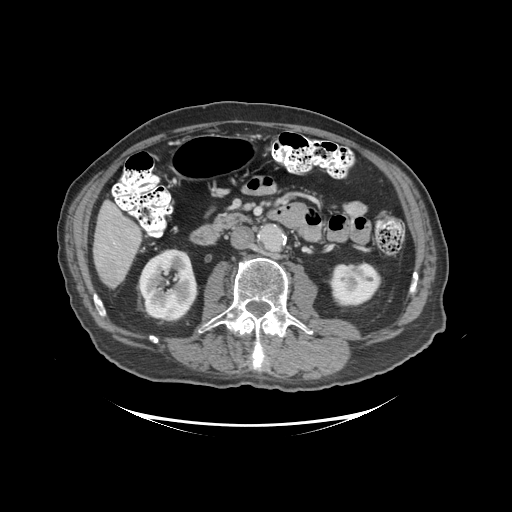
Contrast-enhanced abdominal CT (liver protocol), one axial slice. Position 33 of 99 along the scan axis. Reconstruction kernel STANDARD. 140 kVp. Soft-tissue window (W 400 / L 40 HU). 512 × 512 image matrix, field of view 460 × 460 mm. From the clinical record (not read from this slice): diagnosis: hepatocellular carcinoma (patient treated with transarterial chemoembolisation; whether this scan precedes or follows treatment is not stated here); TNM stage (as recorded): Stage-I; Child-Pugh class: A; tumour differentiation: moderately differentiated; tumour nodularity: uninodular.
Annotated regions visible in this slice (semi-automatic segmentation, software-assisted and operator-edited):
- liver parenchyma outside the tumour (the mass and vessels are separate outlines, so this box may not span the whole liver): box from (x=92, y=200) to (x=140, y=288) px